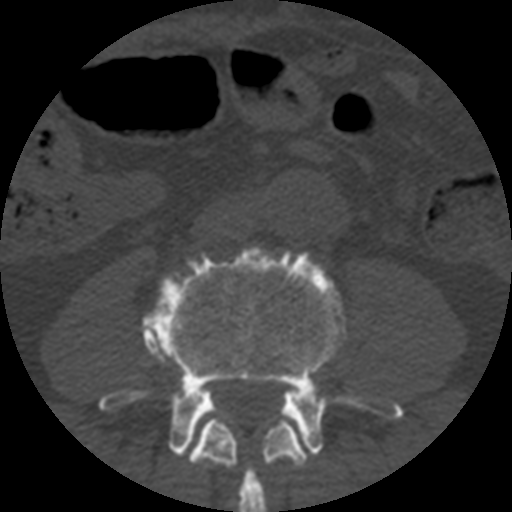
CT including the spine, one axial slice. Slice 101 of 508 in the series (ordered by position). Reconstruction kernel STANDARD. Bone window (W 1800 / L 400 HU). 512 × 512 image matrix. Patient age 57 years. Case-level facts recorded for this patient, not image findings: primary cancer: prostate.
Structures marked on this image (semi-automatic segmentation, software-assisted and operator-edited):
- L3 vertebra: bounding box (x1, y1, x2, y2) in pixels: (189, 418, 307, 512)
- L4 vertebra: (99, 246, 403, 458)